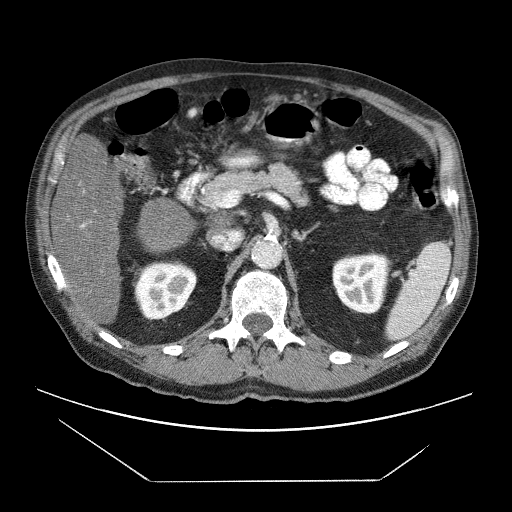
Contrast-enhanced abdominal CT (liver protocol), one axial slice; position 26 of 83 along the scan axis; reconstruction kernel STANDARD; 120 kVp; soft-tissue window (W 400 / L 40 HU); 512 × 512 image matrix. Case-level facts recorded for this patient, not image findings: diagnosis: hepatocellular carcinoma (patient treated with transarterial chemoembolisation; whether this scan precedes or follows treatment is not stated here); TNM stage (as recorded): Stage-IVB; Child-Pugh class: B; tumour nodularity: uninodular.
Structures marked on this image (semi-automatic segmentation, software-assisted and operator-edited):
- liver parenchyma outside the tumour (the mass and vessels are separate outlines, so this box may not span the whole liver): bounding box (x1, y1, x2, y2) in pixels: (52, 176, 122, 326)
- liver vessels: (67, 223, 86, 287)